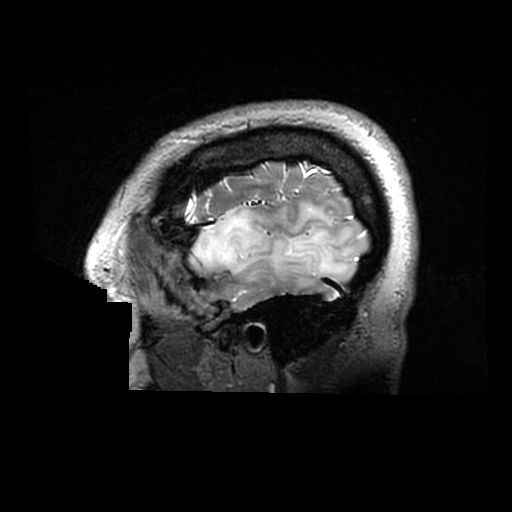
Brain MRI from a brain-tumour surgery series, one sagittal slice; position 248 of 320 along the scan axis; 0.6 mm slice thickness; 512 × 512 image matrix, field of view 240 × 240 mm. Case-level facts recorded for this patient, not image findings: histopathology: Astrocytoma; WHO grade: 2; IDH mutation: yes.
Outlined on this slice (manually delineated by an expert):
- tumour: bounding box [x1, y1, x2, y2] px = [193, 204, 351, 286]